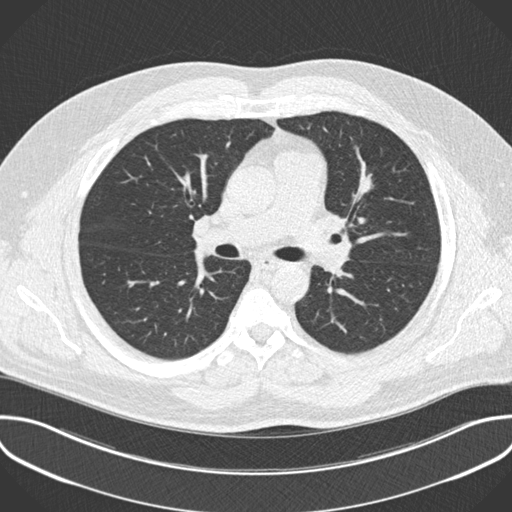
Low-dose screening chest CT, one axial slice. Position 130 of 201 along the scan axis. Lung window (W 1500 / L -600 HU). 2 mm slice thickness. 512 × 512 image matrix, field of view 386 × 386 mm.
Structures marked on this image (manually delineated by an expert):
- lesion 1 (tumor, upper lobe of left lung): bounding box <362,178,372,192> (left, top, right, bottom; pixels)